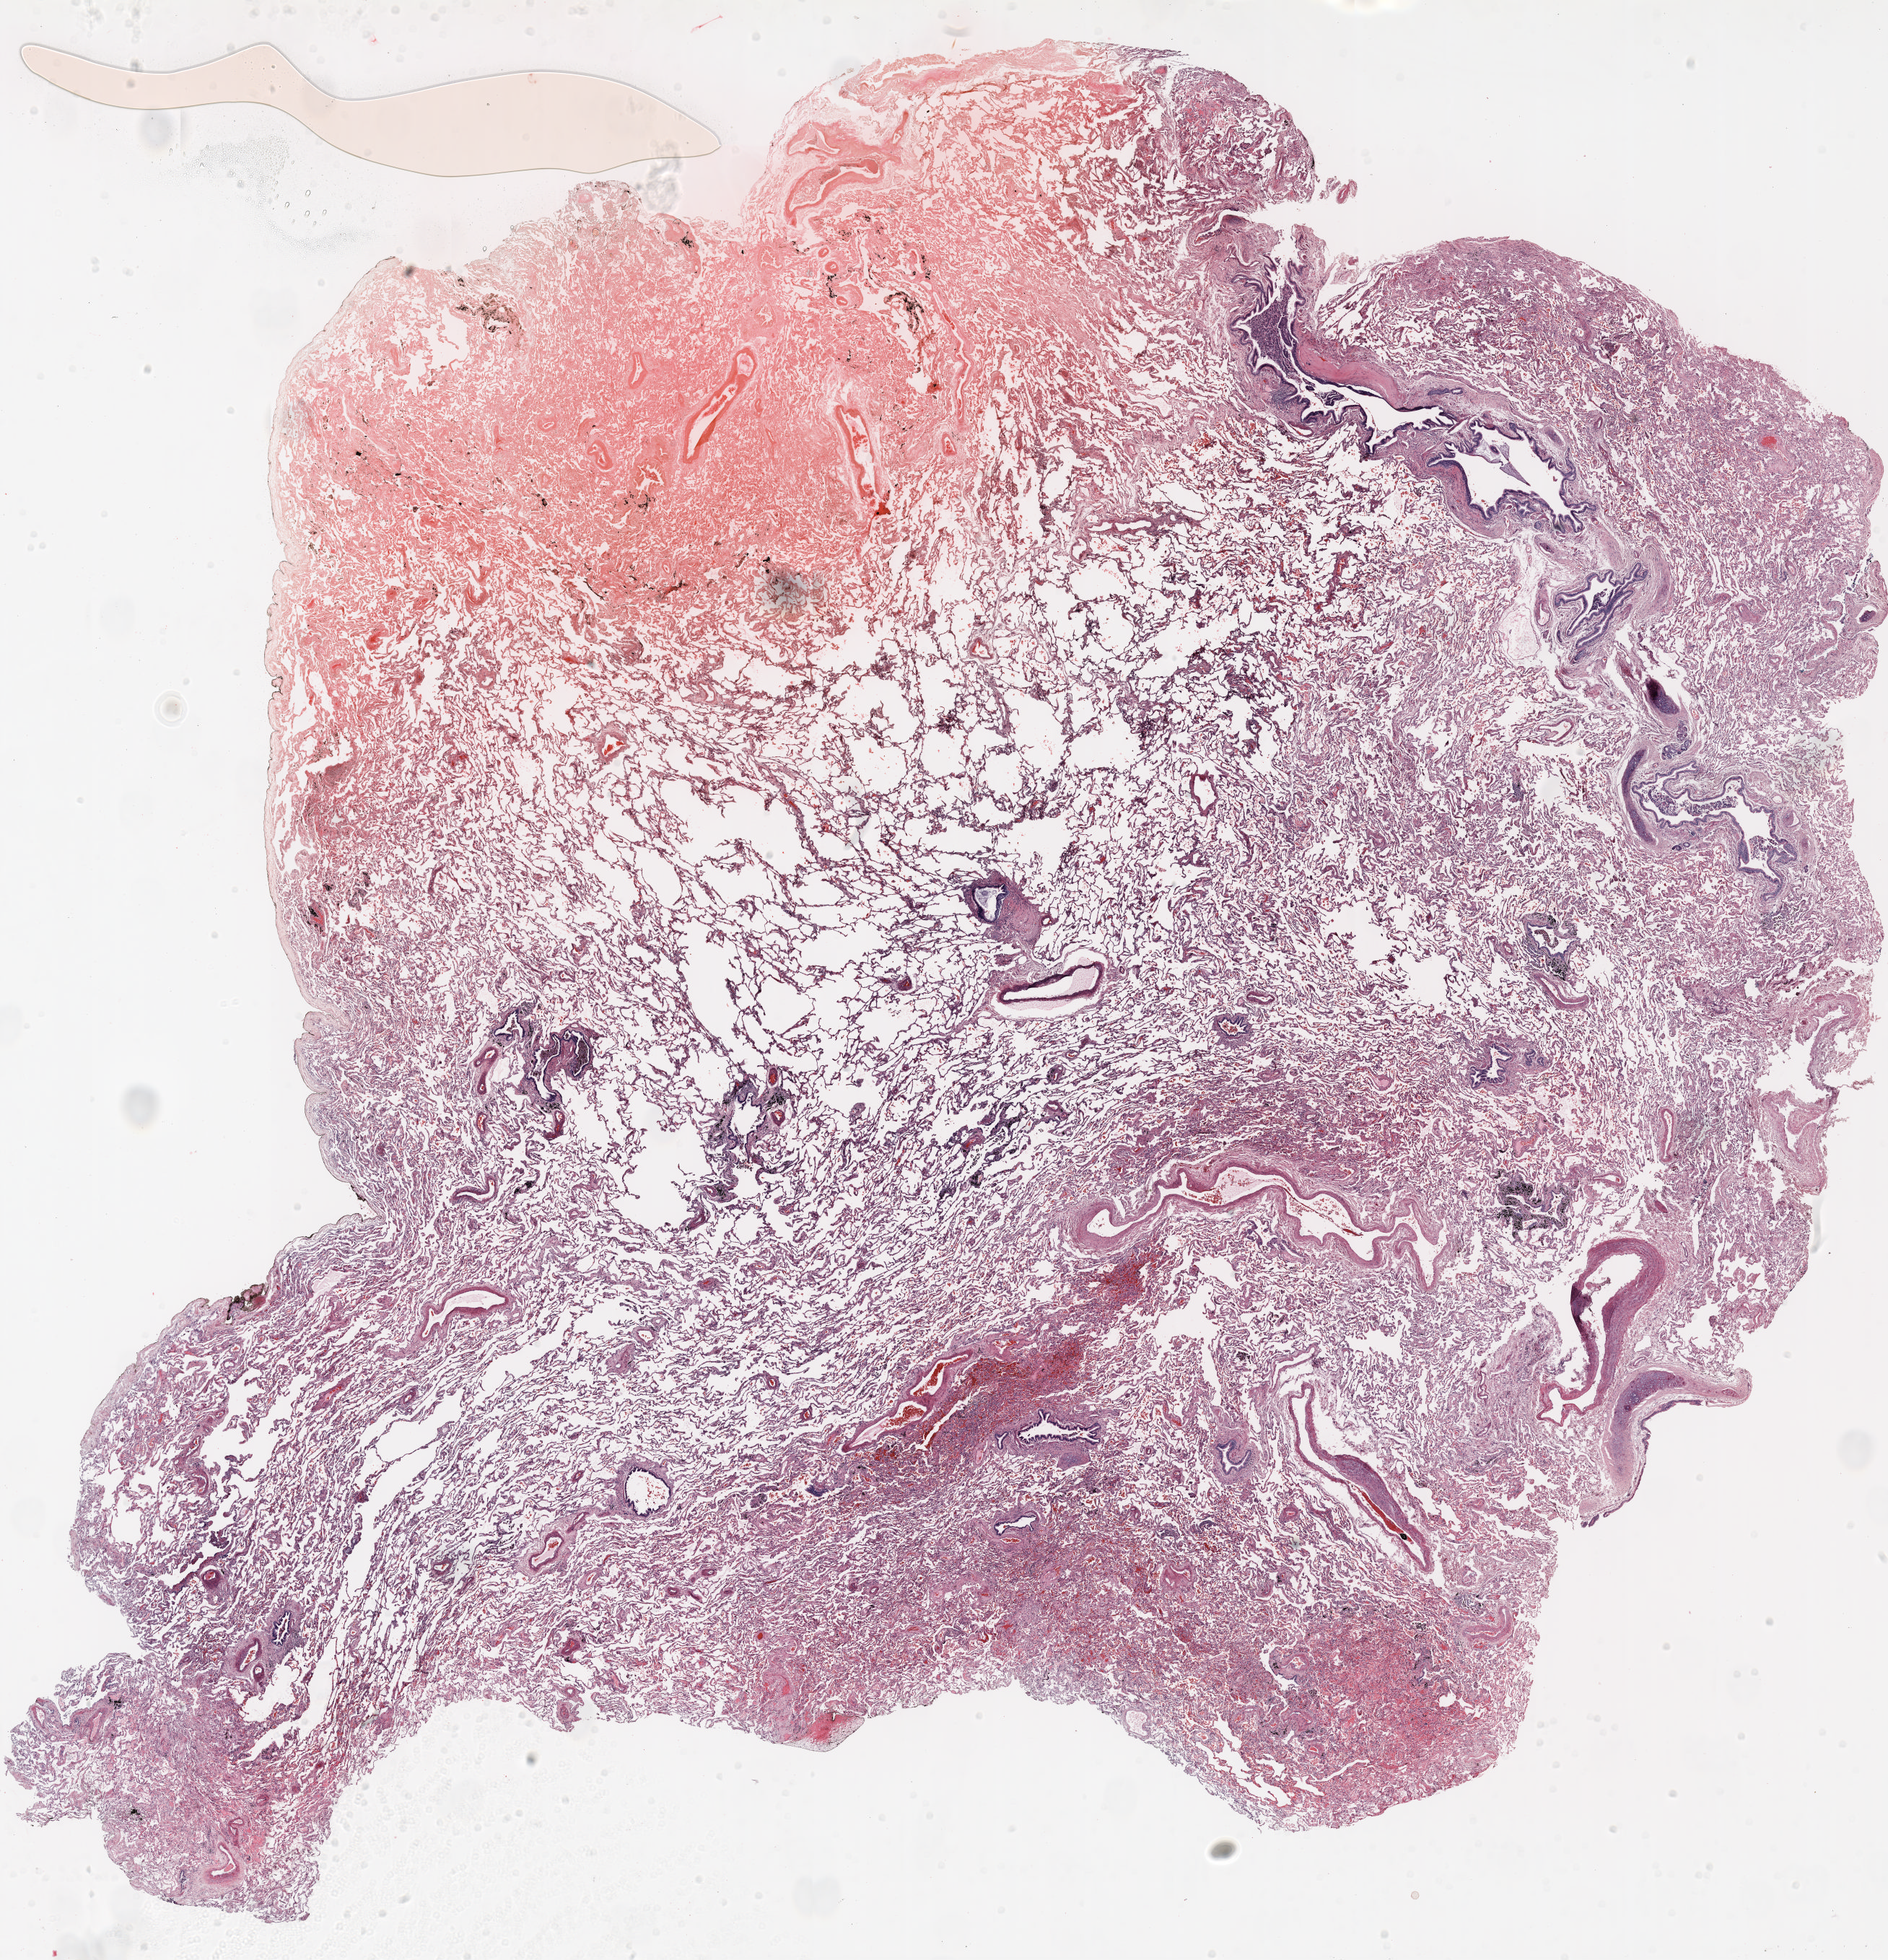
Hematoxylin and eosin (H&E) stained whole-slide image — a low-resolution overview of the entire scanned area, about 21.0 x 21.8 mm; formalin-fixed paraffin-embedded (FFPE) section; lung tissue. Female, age 61 at enrolment. Former smoker at enrolment.
Participant's lung-cancer diagnosis: Adenocarcinoma, NOS. Stage (AJCC 6th edition): IIIB. Primary tumour location (clinical record): left upper lobe. Tumour size (pathology): 15 mm.